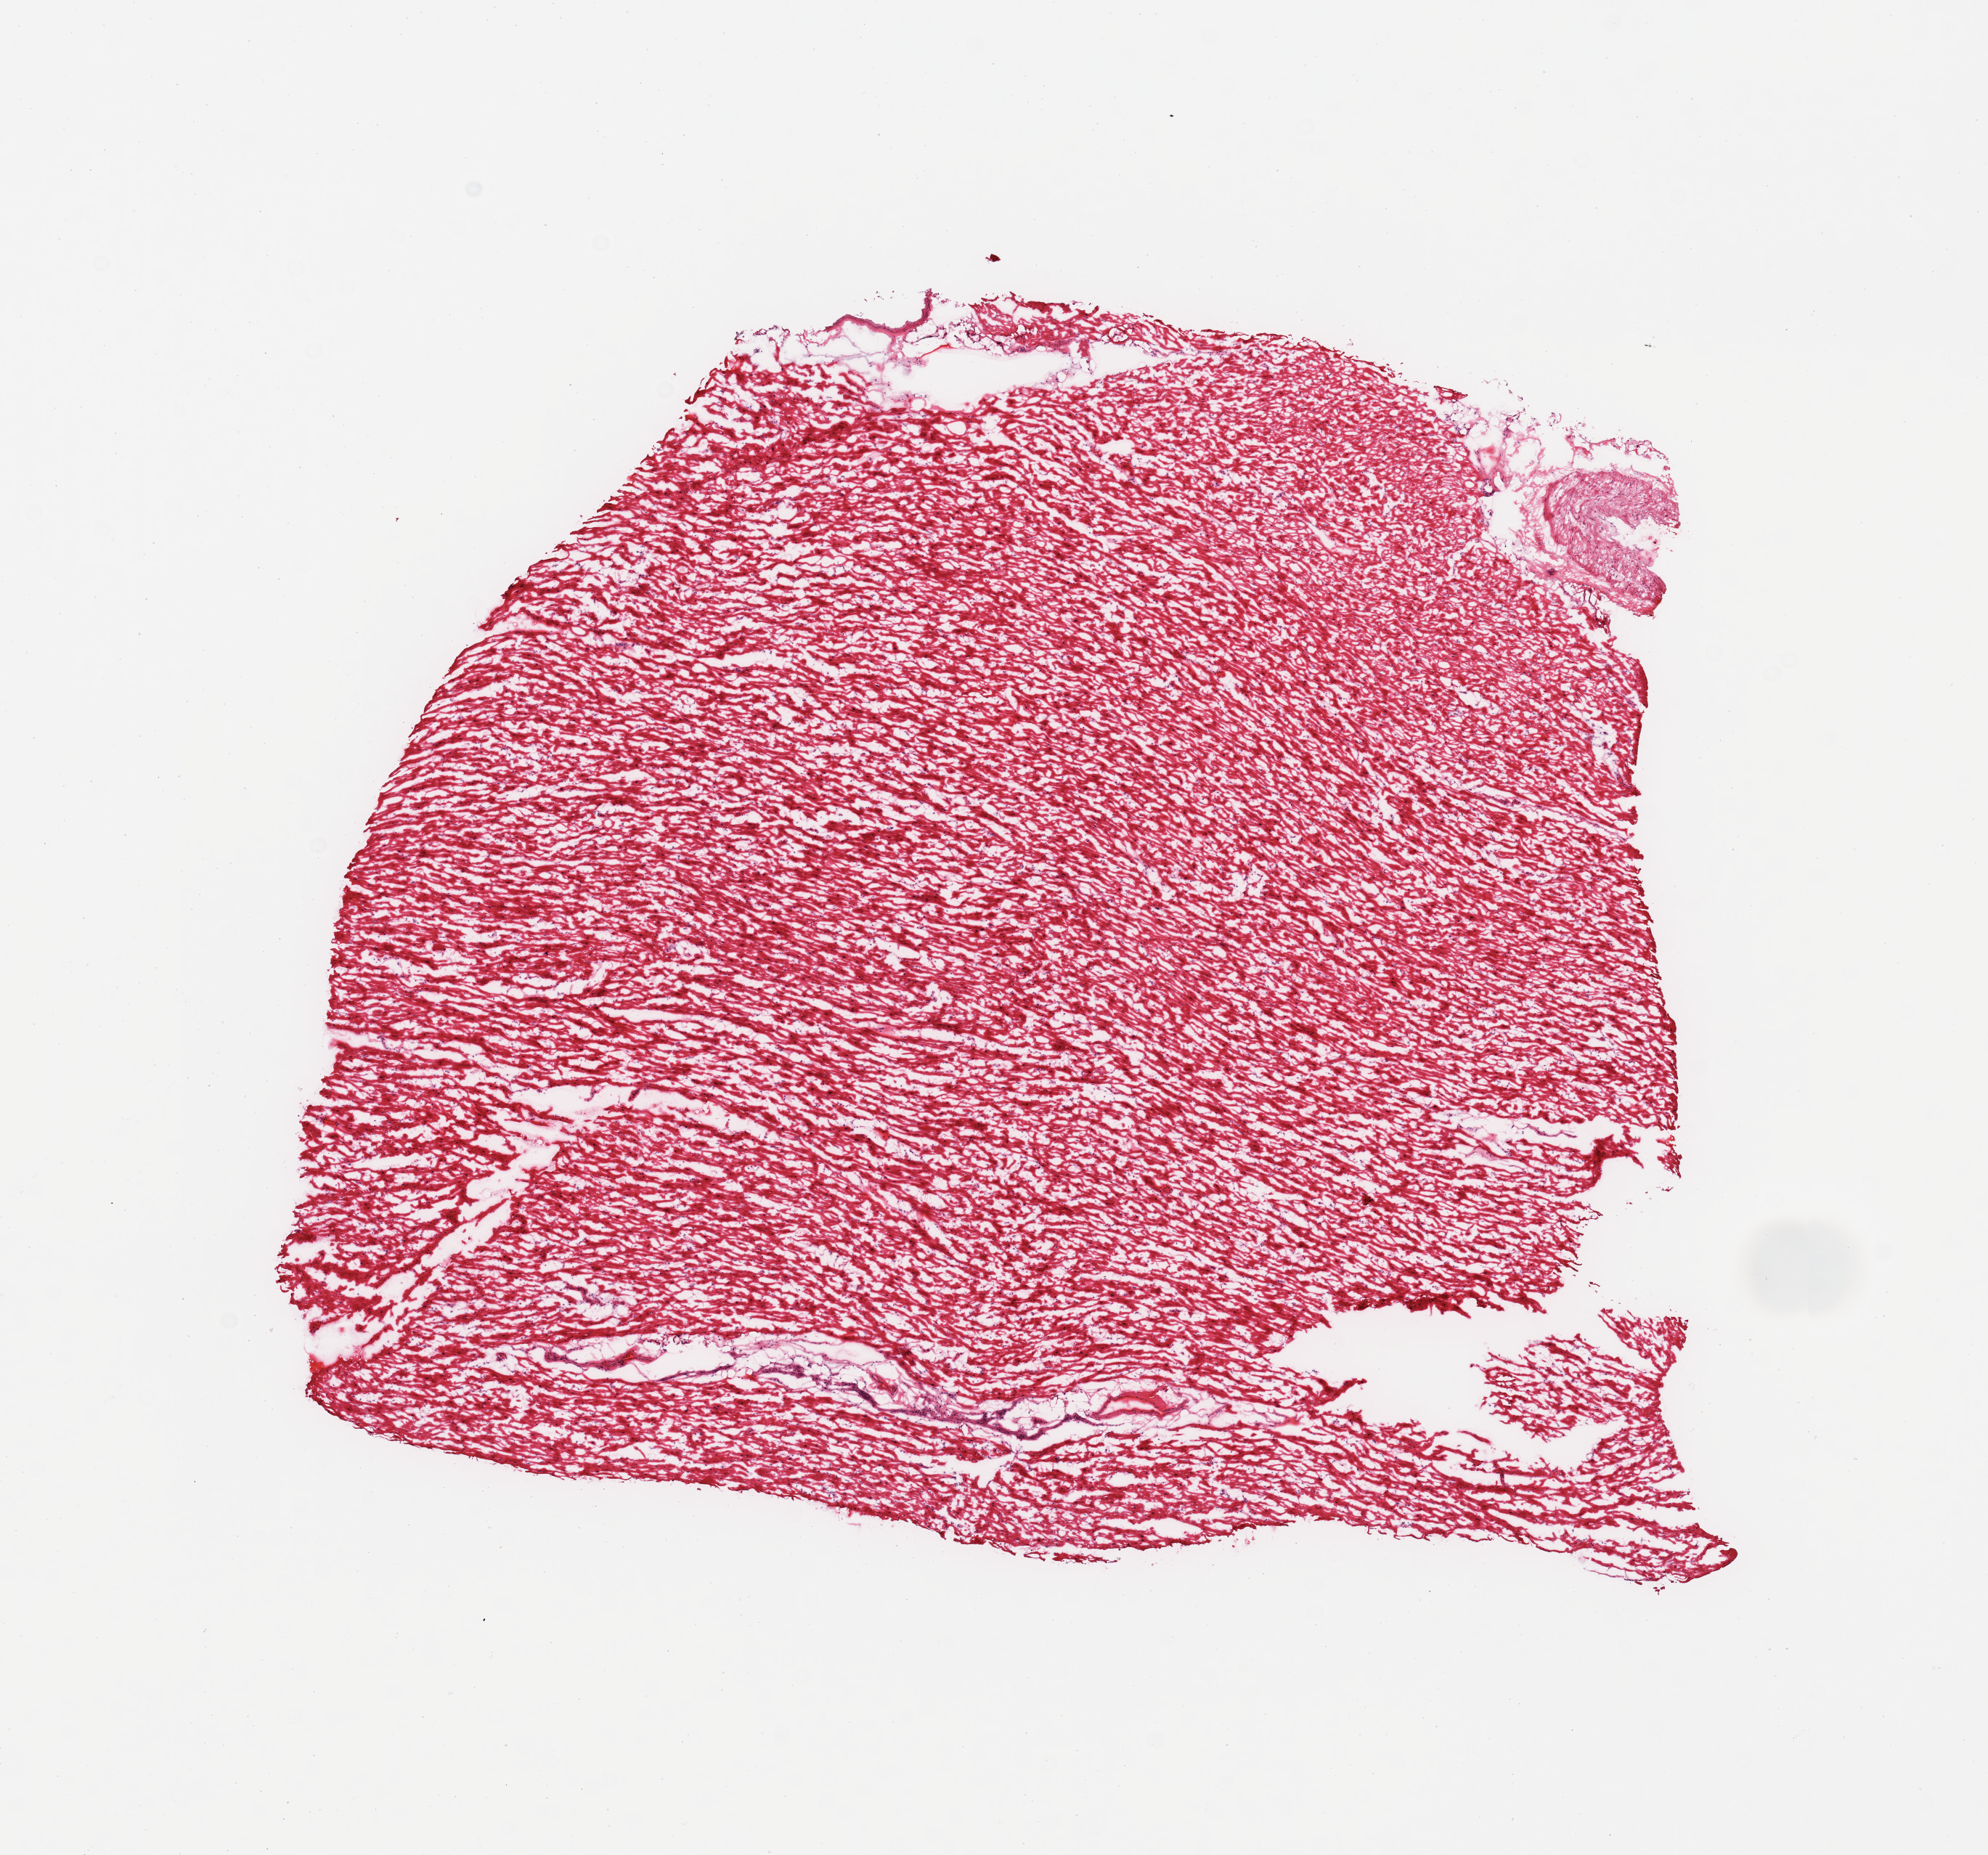
Digitized hematoxylin and eosin (H&E)-stained section, shown as a low-resolution overview of the whole scanned area (about 10.8 x 10.1 mm, slide scanned at 20x), frozen section, sampled site (target tissue): heart, tissue donor sample. Donor: female.
- reviewer comment on this tissue sample: 1 piece; 0.6mm artery at 1 edge